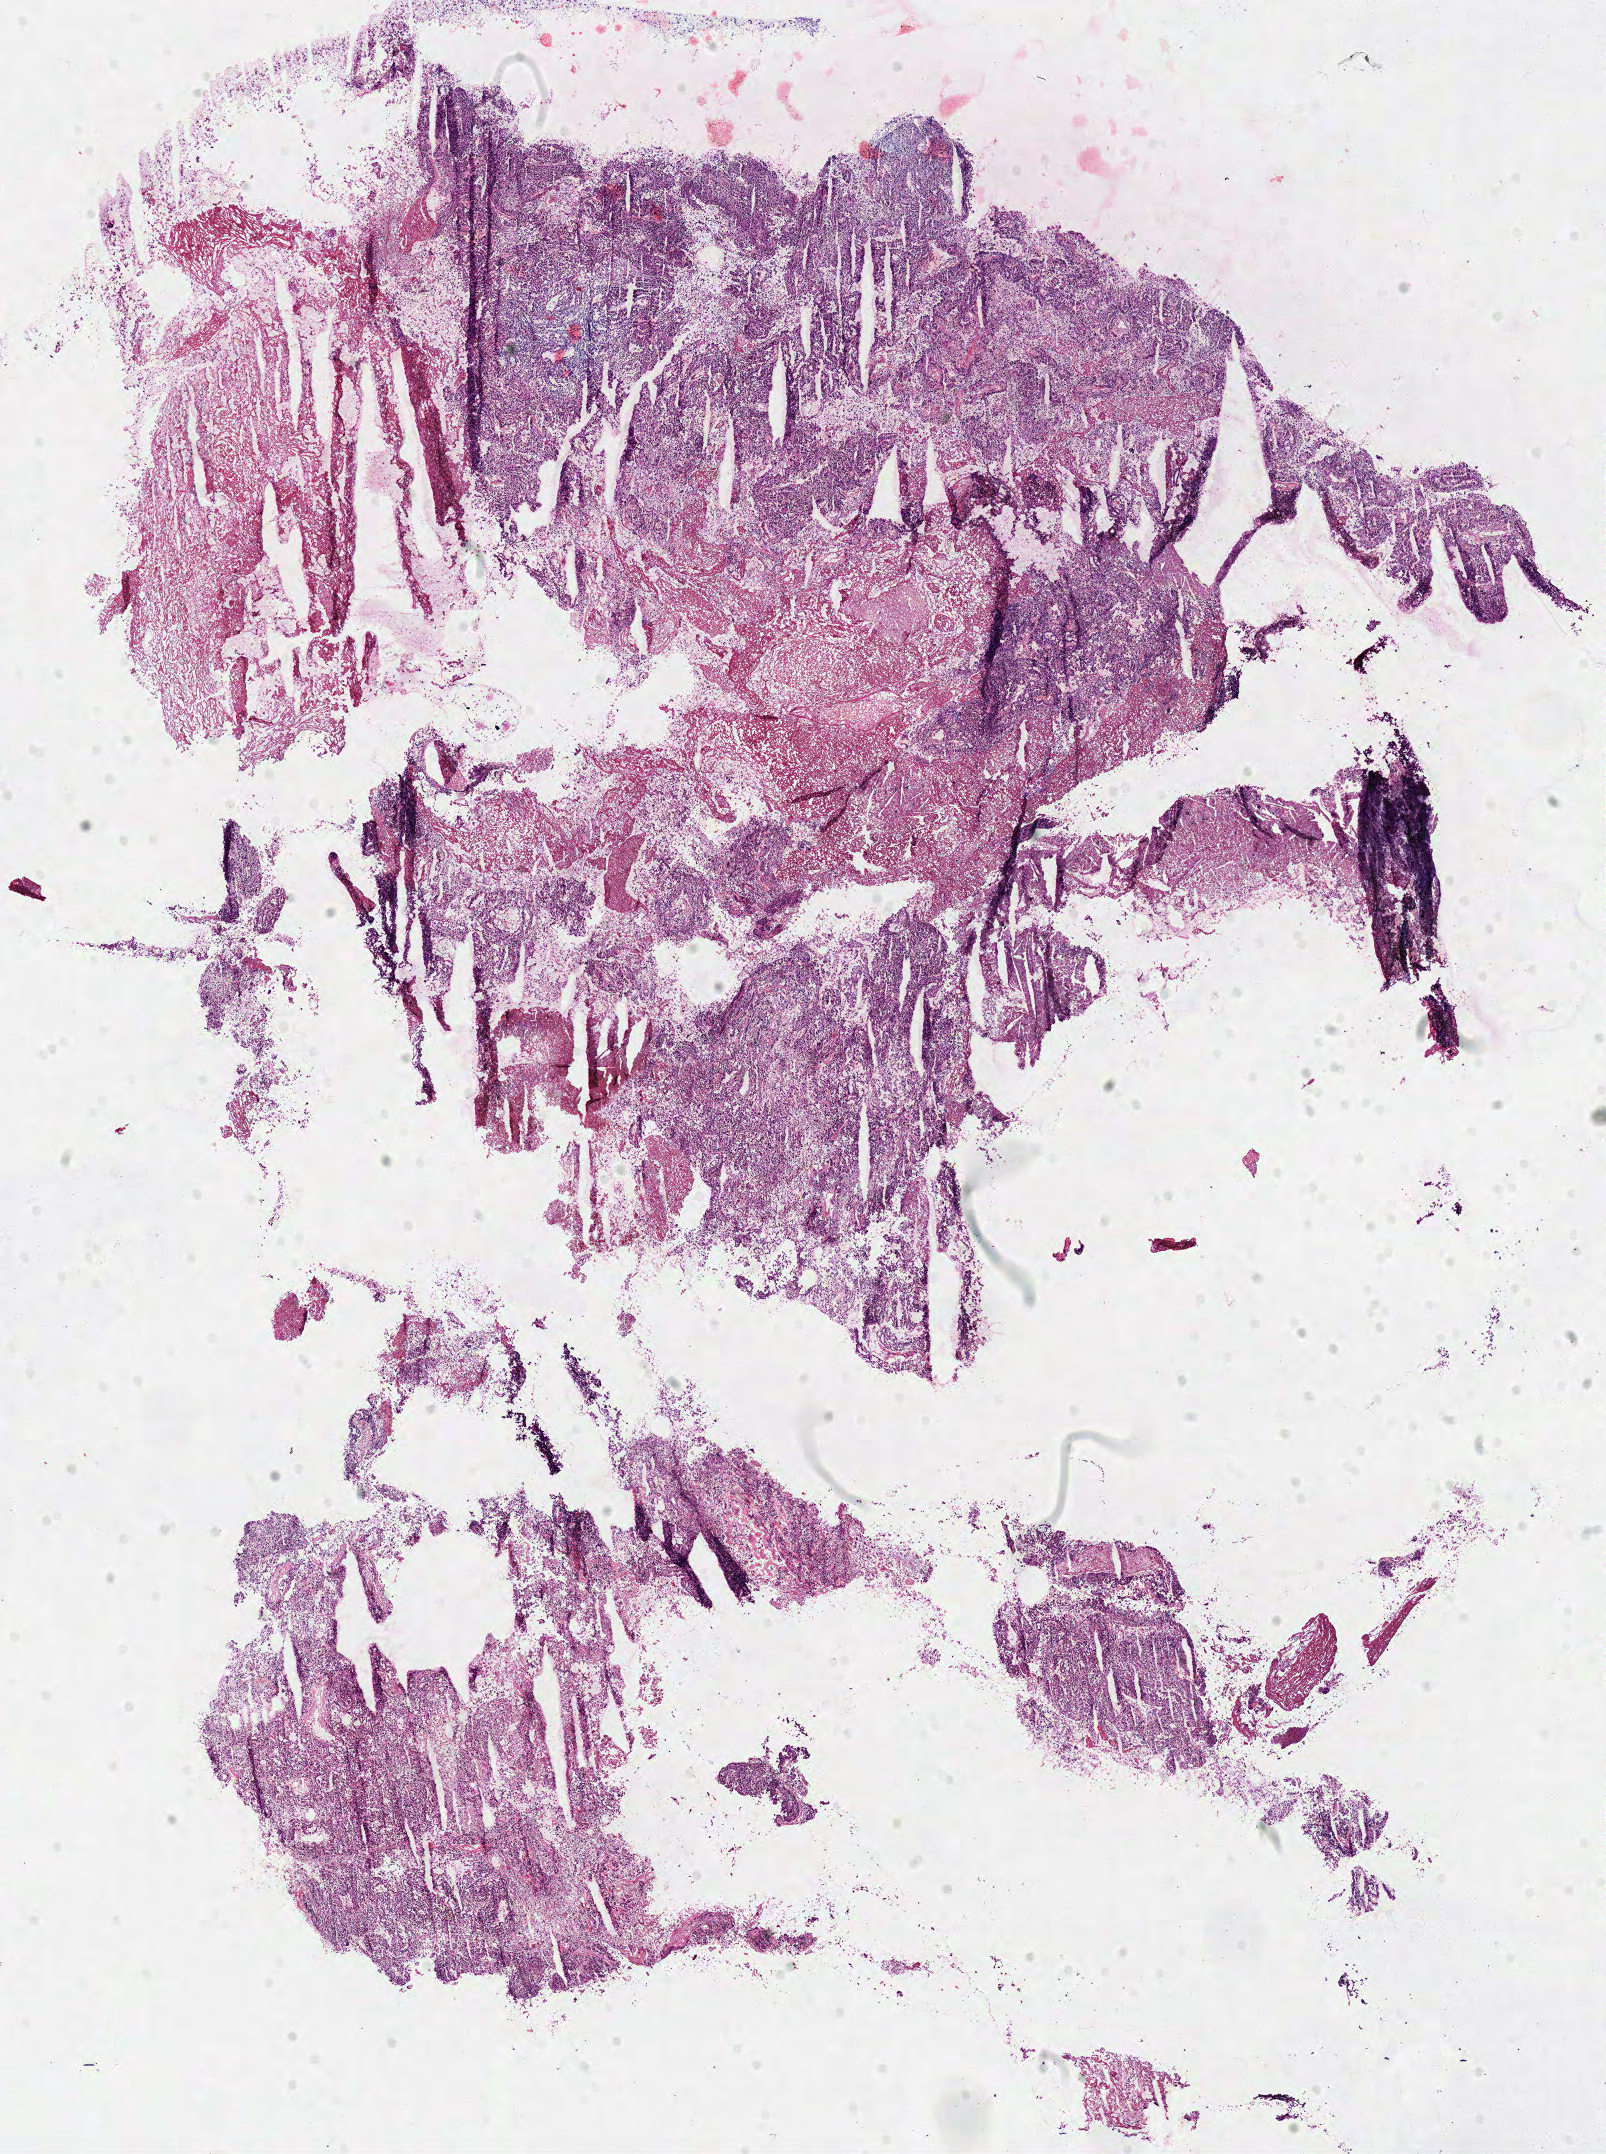
H&E-stained whole-slide image, whole scanned area (about 12.7 x 17.0 mm, slide scanned at 40x) shown as a low-resolution overview. Frozen section. Sample: primary tumour, kidney. Patient: male, age at initial diagnosis 69 years. Slide review estimates, as recorded: tumour cells 65%, tumour nuclei 75%, normal cells 0%, stromal cells 30%, necrosis 5%.
- AJCC pathologic stage: III
- lymph nodes positive (case pathology): 0 of 9 examined
- laterality: right
- diagnosis: Papillary adenocarcinoma, NOS